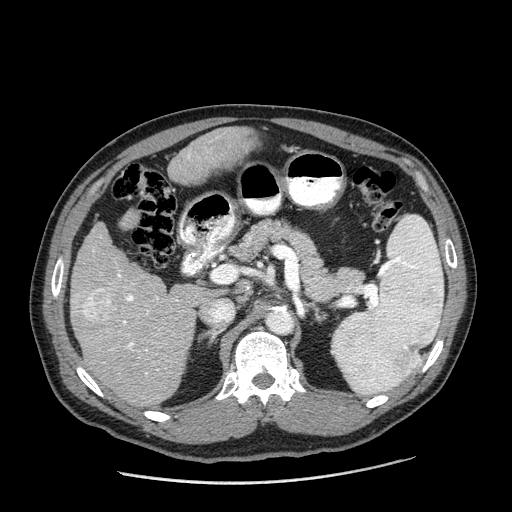
Contrast-enhanced abdominal CT (liver protocol), one axial slice. Position 99 of 198 along the scan axis. Reconstruction kernel STANDARD. One of 2 acquisitions stored at this slice position. Soft-tissue window (W 400 / L 40 HU). 2.5 mm slice thickness. 512 × 512 image matrix, field of view 400 × 400 mm. Case-level facts recorded for this patient, not image findings: diagnosis: hepatocellular carcinoma (patient treated with transarterial chemoembolisation; whether this scan precedes or follows treatment is not stated here); TNM stage (as recorded): Stage-II; Child-Pugh class: A; tumour differentiation: moderately differentiated; tumour nodularity: multinodular.
Structures marked on this image (semi-automatically segmented with operator editing):
- liver parenchyma outside the tumour (the mass and vessels are separate outlines, so this box may not span the whole liver): bounding box <70,126,254,406> (left, top, right, bottom; pixels)
- mass: <83,287,119,328>
- liver vessels: <110,156,190,375>